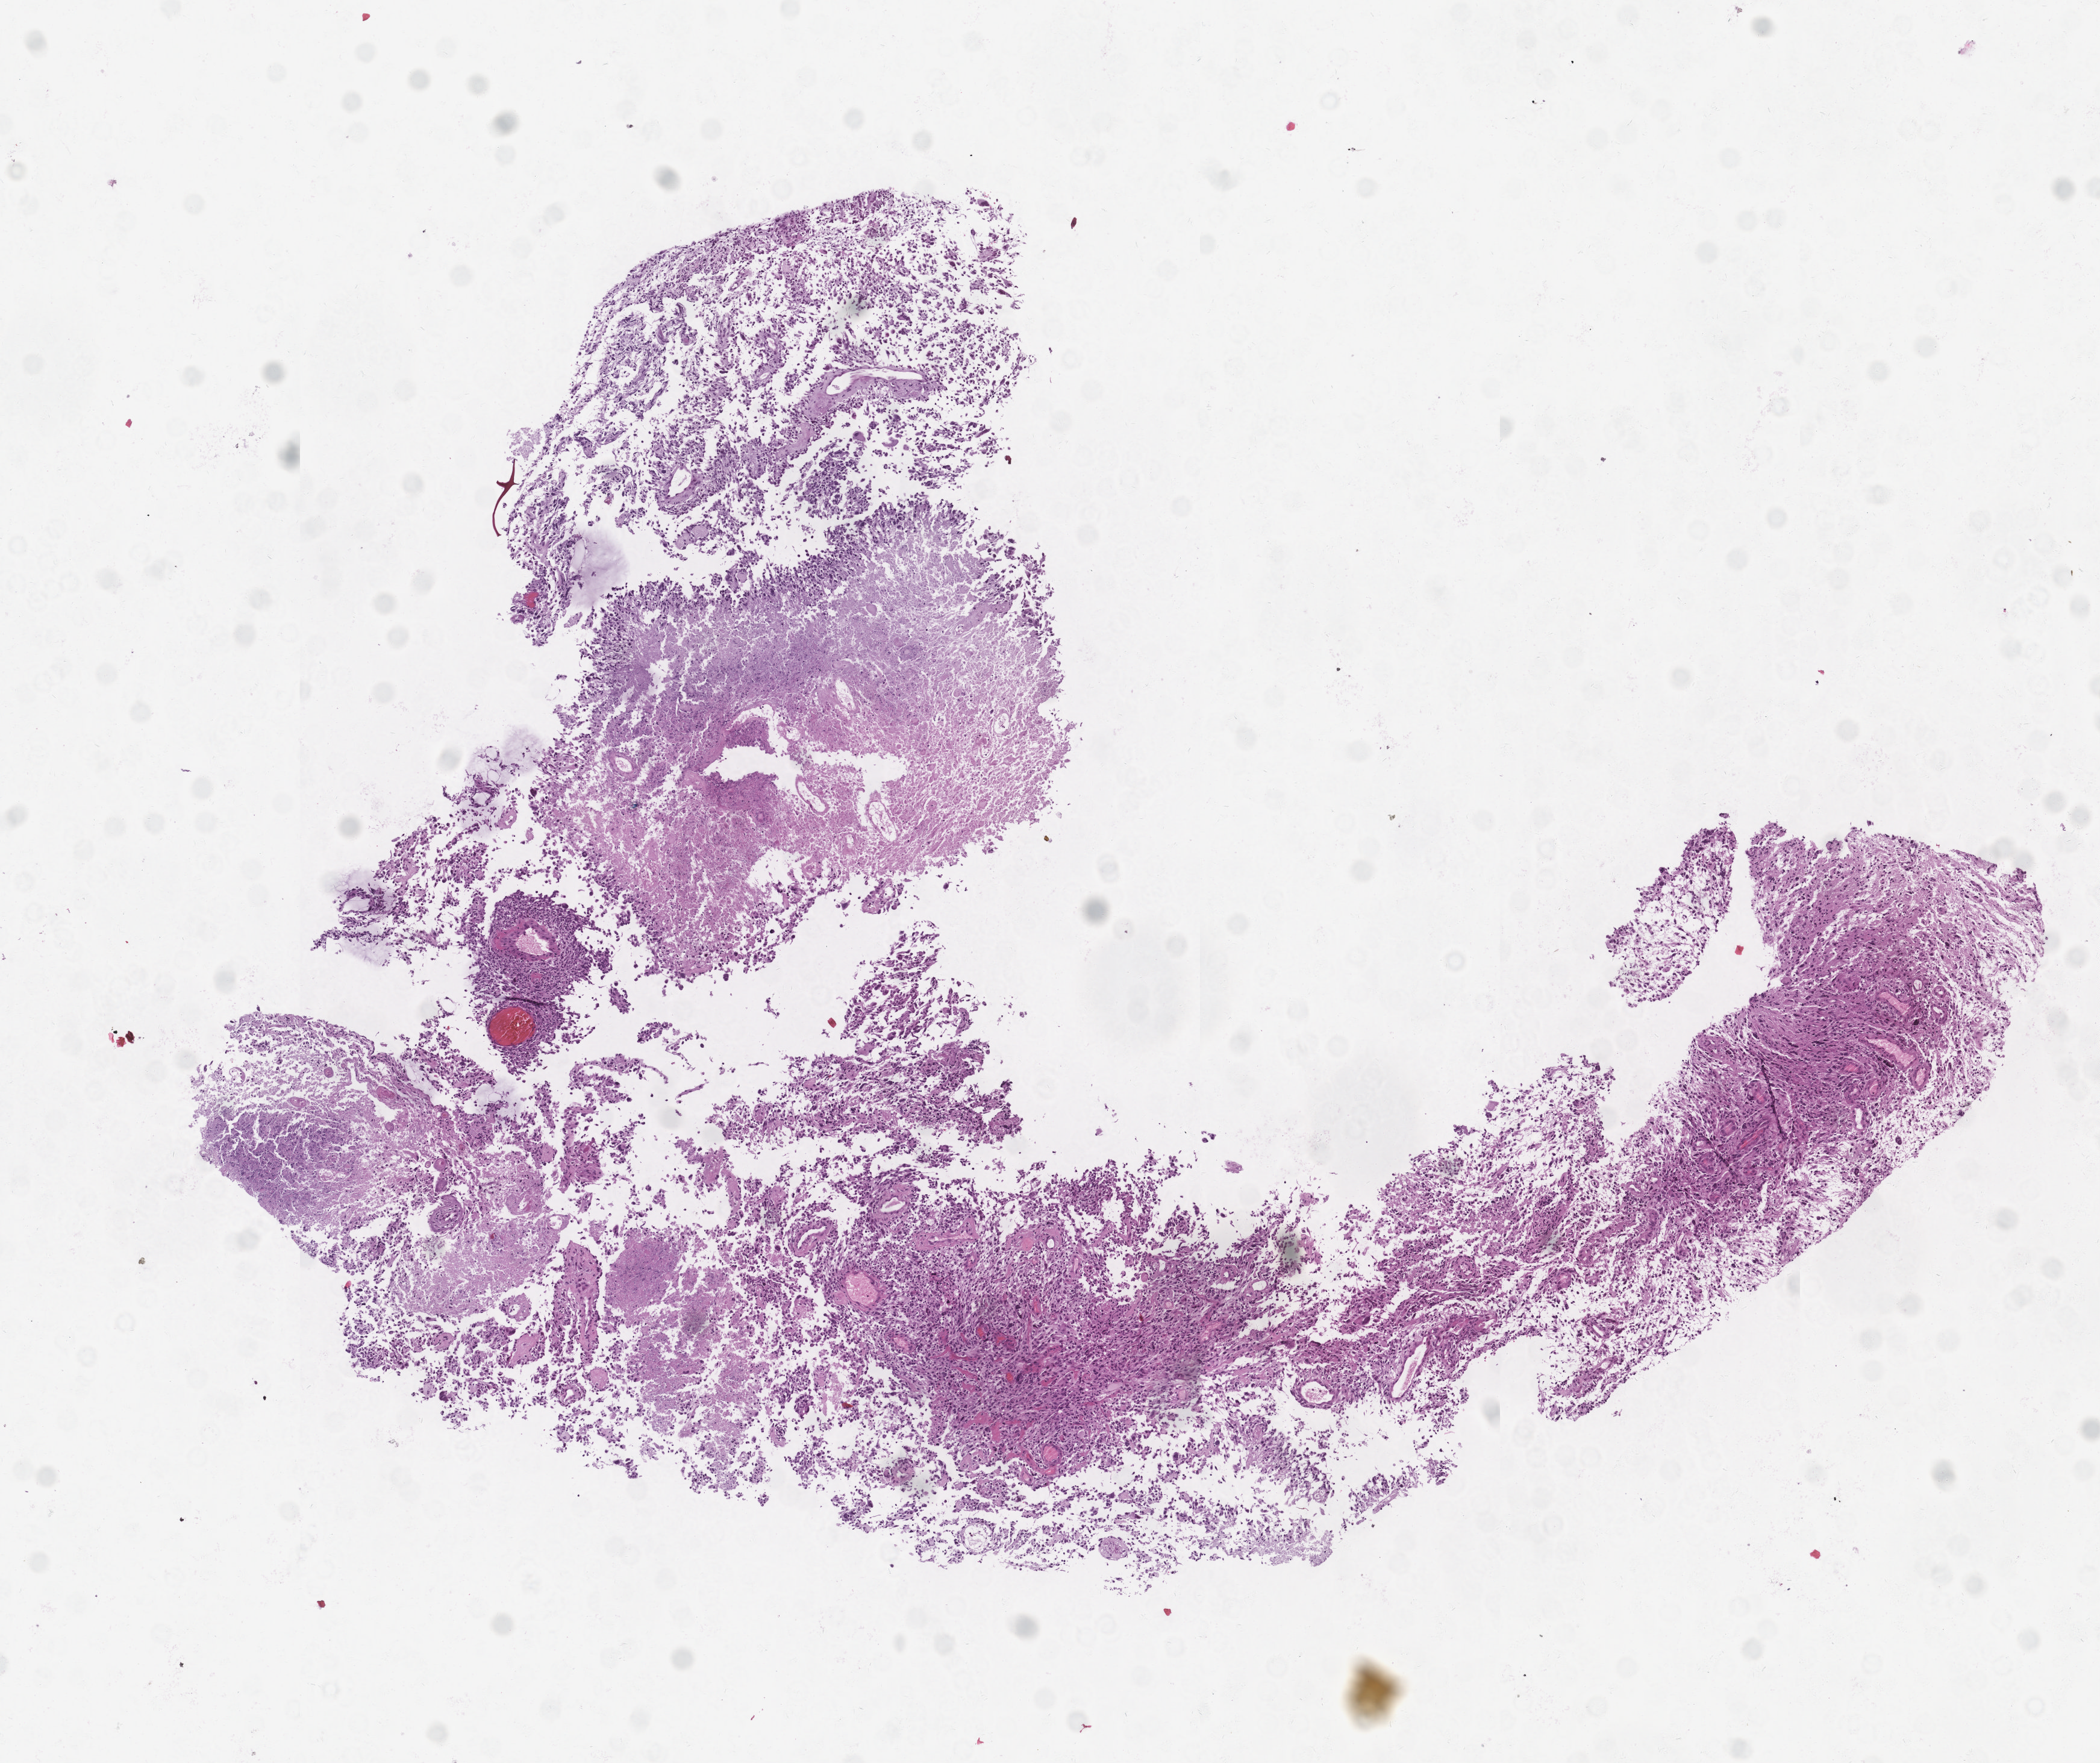
Hematoxylin and eosin (H&E) stained whole-slide image, a low-resolution overview of the entire scanned area, about 7.0 x 5.9 mm (from a 20x scan); brain, tumour tissue. 31-year-old male patient.
Diagnosis: Glioblastoma.